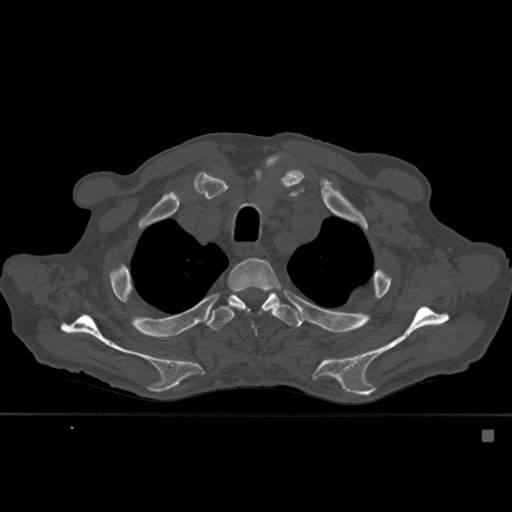
CT including the spine, one axial slice. Slice 425 of 527 in the series (ordered by position). Bone window (W 1800 / L 400 HU). 1.5 mm slice thickness. 512 × 512 image matrix, field of view 373 × 373 mm. Male patient, age 78 years. From the clinical record (not read from this slice): primary cancer: prostate.
Annotated regions visible in this slice (semi-automatic segmentation, software-assisted and operator-edited):
- T3 vertebra: bounding box [x1, y1, x2, y2] px = [227, 258, 282, 315]
- T4 vertebra: [207, 286, 302, 331]